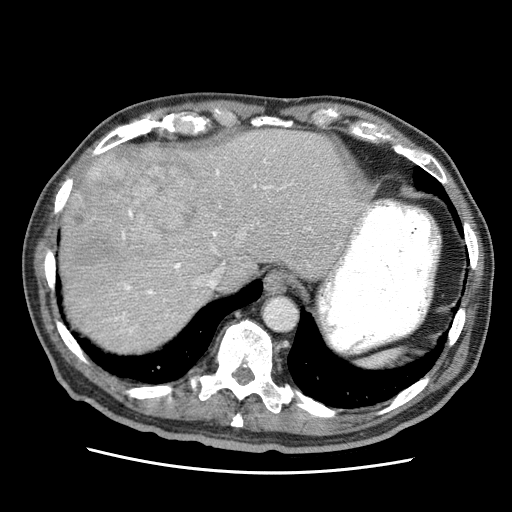
Contrast-enhanced abdominal CT (liver protocol), one axial slice. Slice 52 of 75 in the series (ordered by position). Reconstruction kernel STANDARD. Soft-tissue window (W 400 / L 40 HU). 512 × 512 image matrix, field of view 360 × 360 mm. Case-level facts recorded for this patient, not image findings: diagnosis: hepatocellular carcinoma (patient treated with transarterial chemoembolisation; whether this scan precedes or follows treatment is not stated here); TNM stage (as recorded): Stage-IIIA; Child-Pugh class: A; tumour differentiation: well differentiated; tumour size: 13.9 cm.
Annotated regions visible in this slice (semi-automatic segmentation, software-assisted and operator-edited):
- abdominal aorta: box from (x=266, y=297) to (x=297, y=330) px
- liver parenchyma outside the tumour (the mass and vessels are separate outlines, so this box may not span the whole liver): (x=62, y=129)–(x=366, y=352)
- mass: (x=59, y=148)–(x=202, y=284)
- liver vessels: (x=109, y=159)–(x=311, y=334)